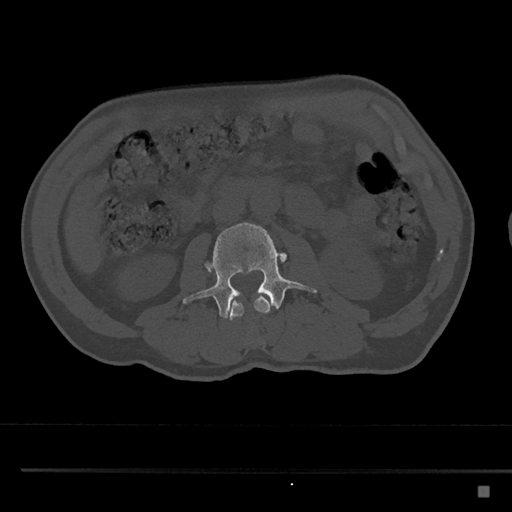
CT including the spine, one axial slice; position 714 of 797 along the scan axis; reconstruction kernel Br40s/3; 120 kVp; bone window (W 1800 / L 400 HU); 512 × 512 image matrix, field of view 391 × 391 mm. Patient: male, 59 years. From the clinical record (not read from this slice): primary cancer: prostate.
Structures marked on this image (semi-automatic segmentation, software-assisted and operator-edited):
- L2 vertebra: box from (x=228, y=295) to (x=270, y=320) px
- L3 vertebra: (x=182, y=222)–(x=317, y=318)